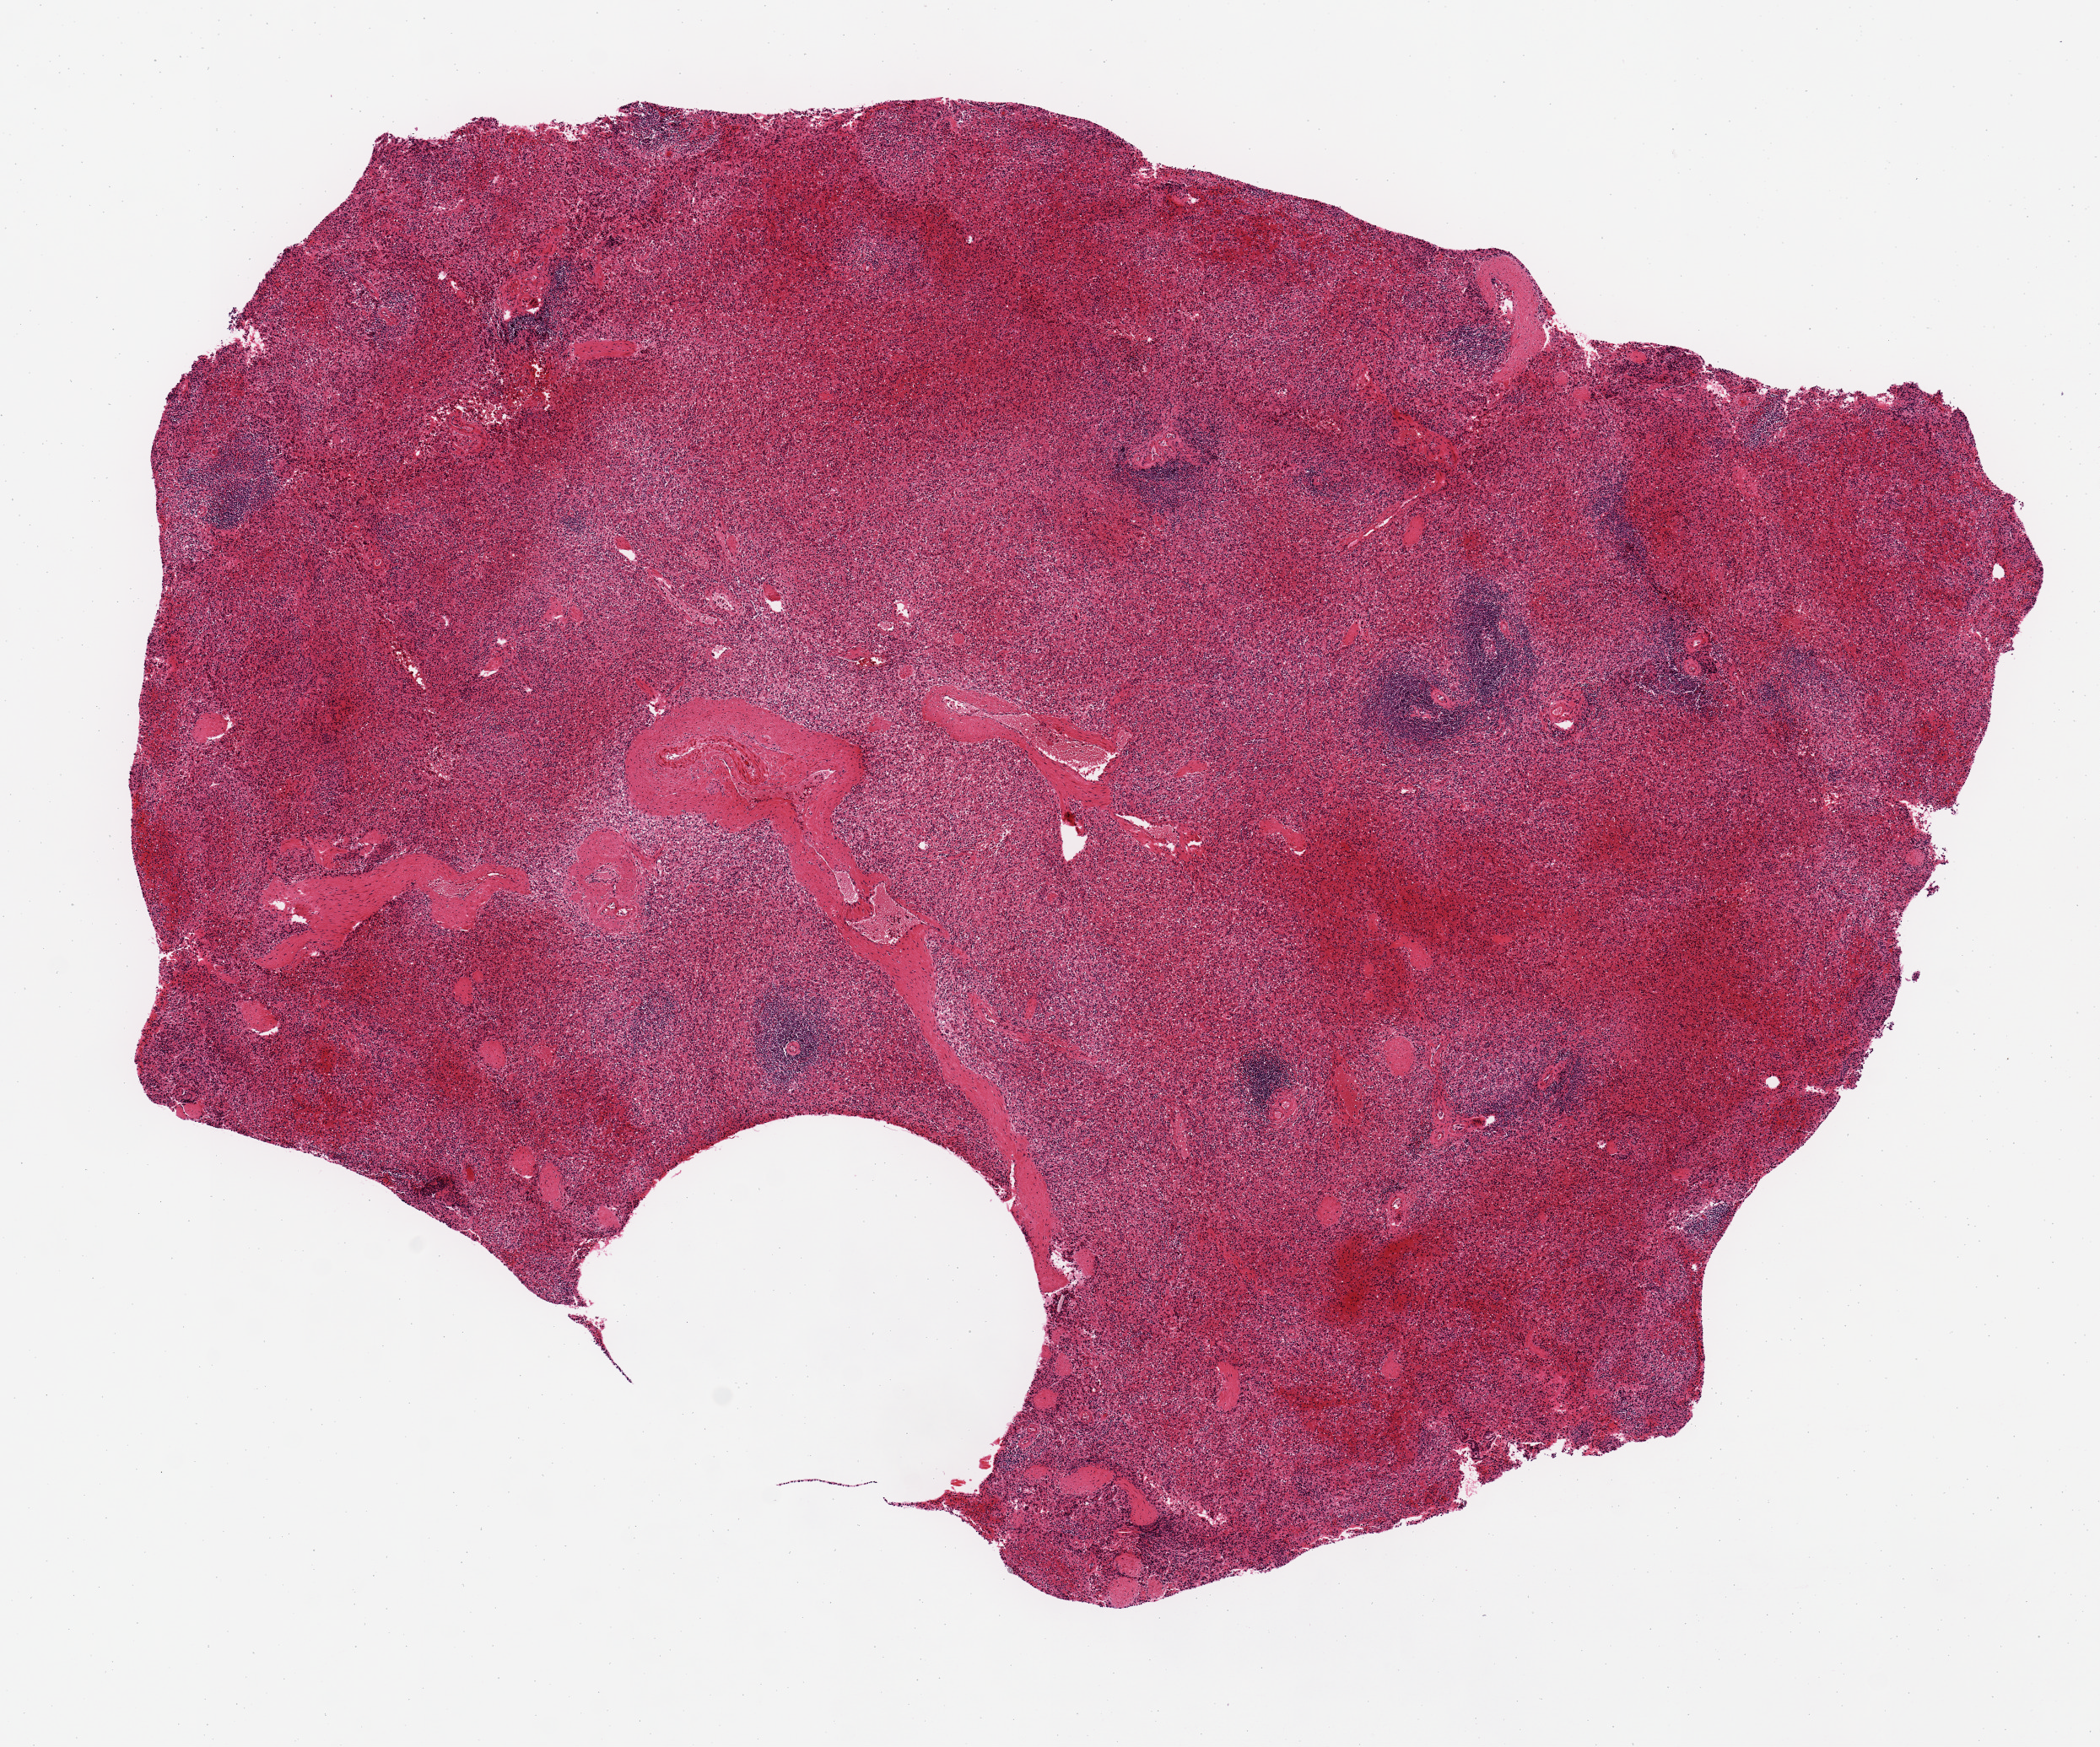
Digitized hematoxylin and eosin (H&E)-stained section, shown as a low-resolution overview of the whole scanned area (about 9.8 x 8.2 mm, slide scanned at 20x). PAXgene-fixed paraffin-embedded (PFPE) section. Sampled site (target tissue): spleen. Donor tissue sample. Donor: male.
Reviewer comment on this tissue sample: 2-3. 8.4x5.8mm.